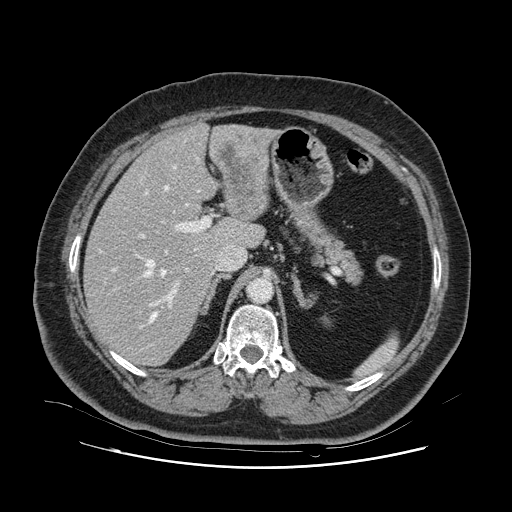
Contrast-enhanced abdominal CT, one axial slice. Position 70 of 132 along the scan axis. Intravenous contrast given. Soft-tissue window (W 400 / L 40 HU). 2.5 mm slice thickness. 512 × 512 image matrix, field of view 391 × 391 mm. Female patient, age 73 years. From the clinical record (not read from this slice): diagnosis: colorectal cancer liver metastases, imaged before liver resection; multiple liver metastases: no; largest metastasis: 7 cm; disease in both lobes: no.
Structures marked on this image (expert manual segmentation):
- hepatic veins: bounding box [x1, y1, x2, y2] px = [99, 165, 200, 328]
- liver: [85, 125, 272, 366]
- planned liver remnant (the part of the liver to remain after resection): [85, 154, 243, 366]
- portal vein (with intrahepatic branches): [113, 191, 211, 308]
- liver metastasis: [219, 146, 257, 208]